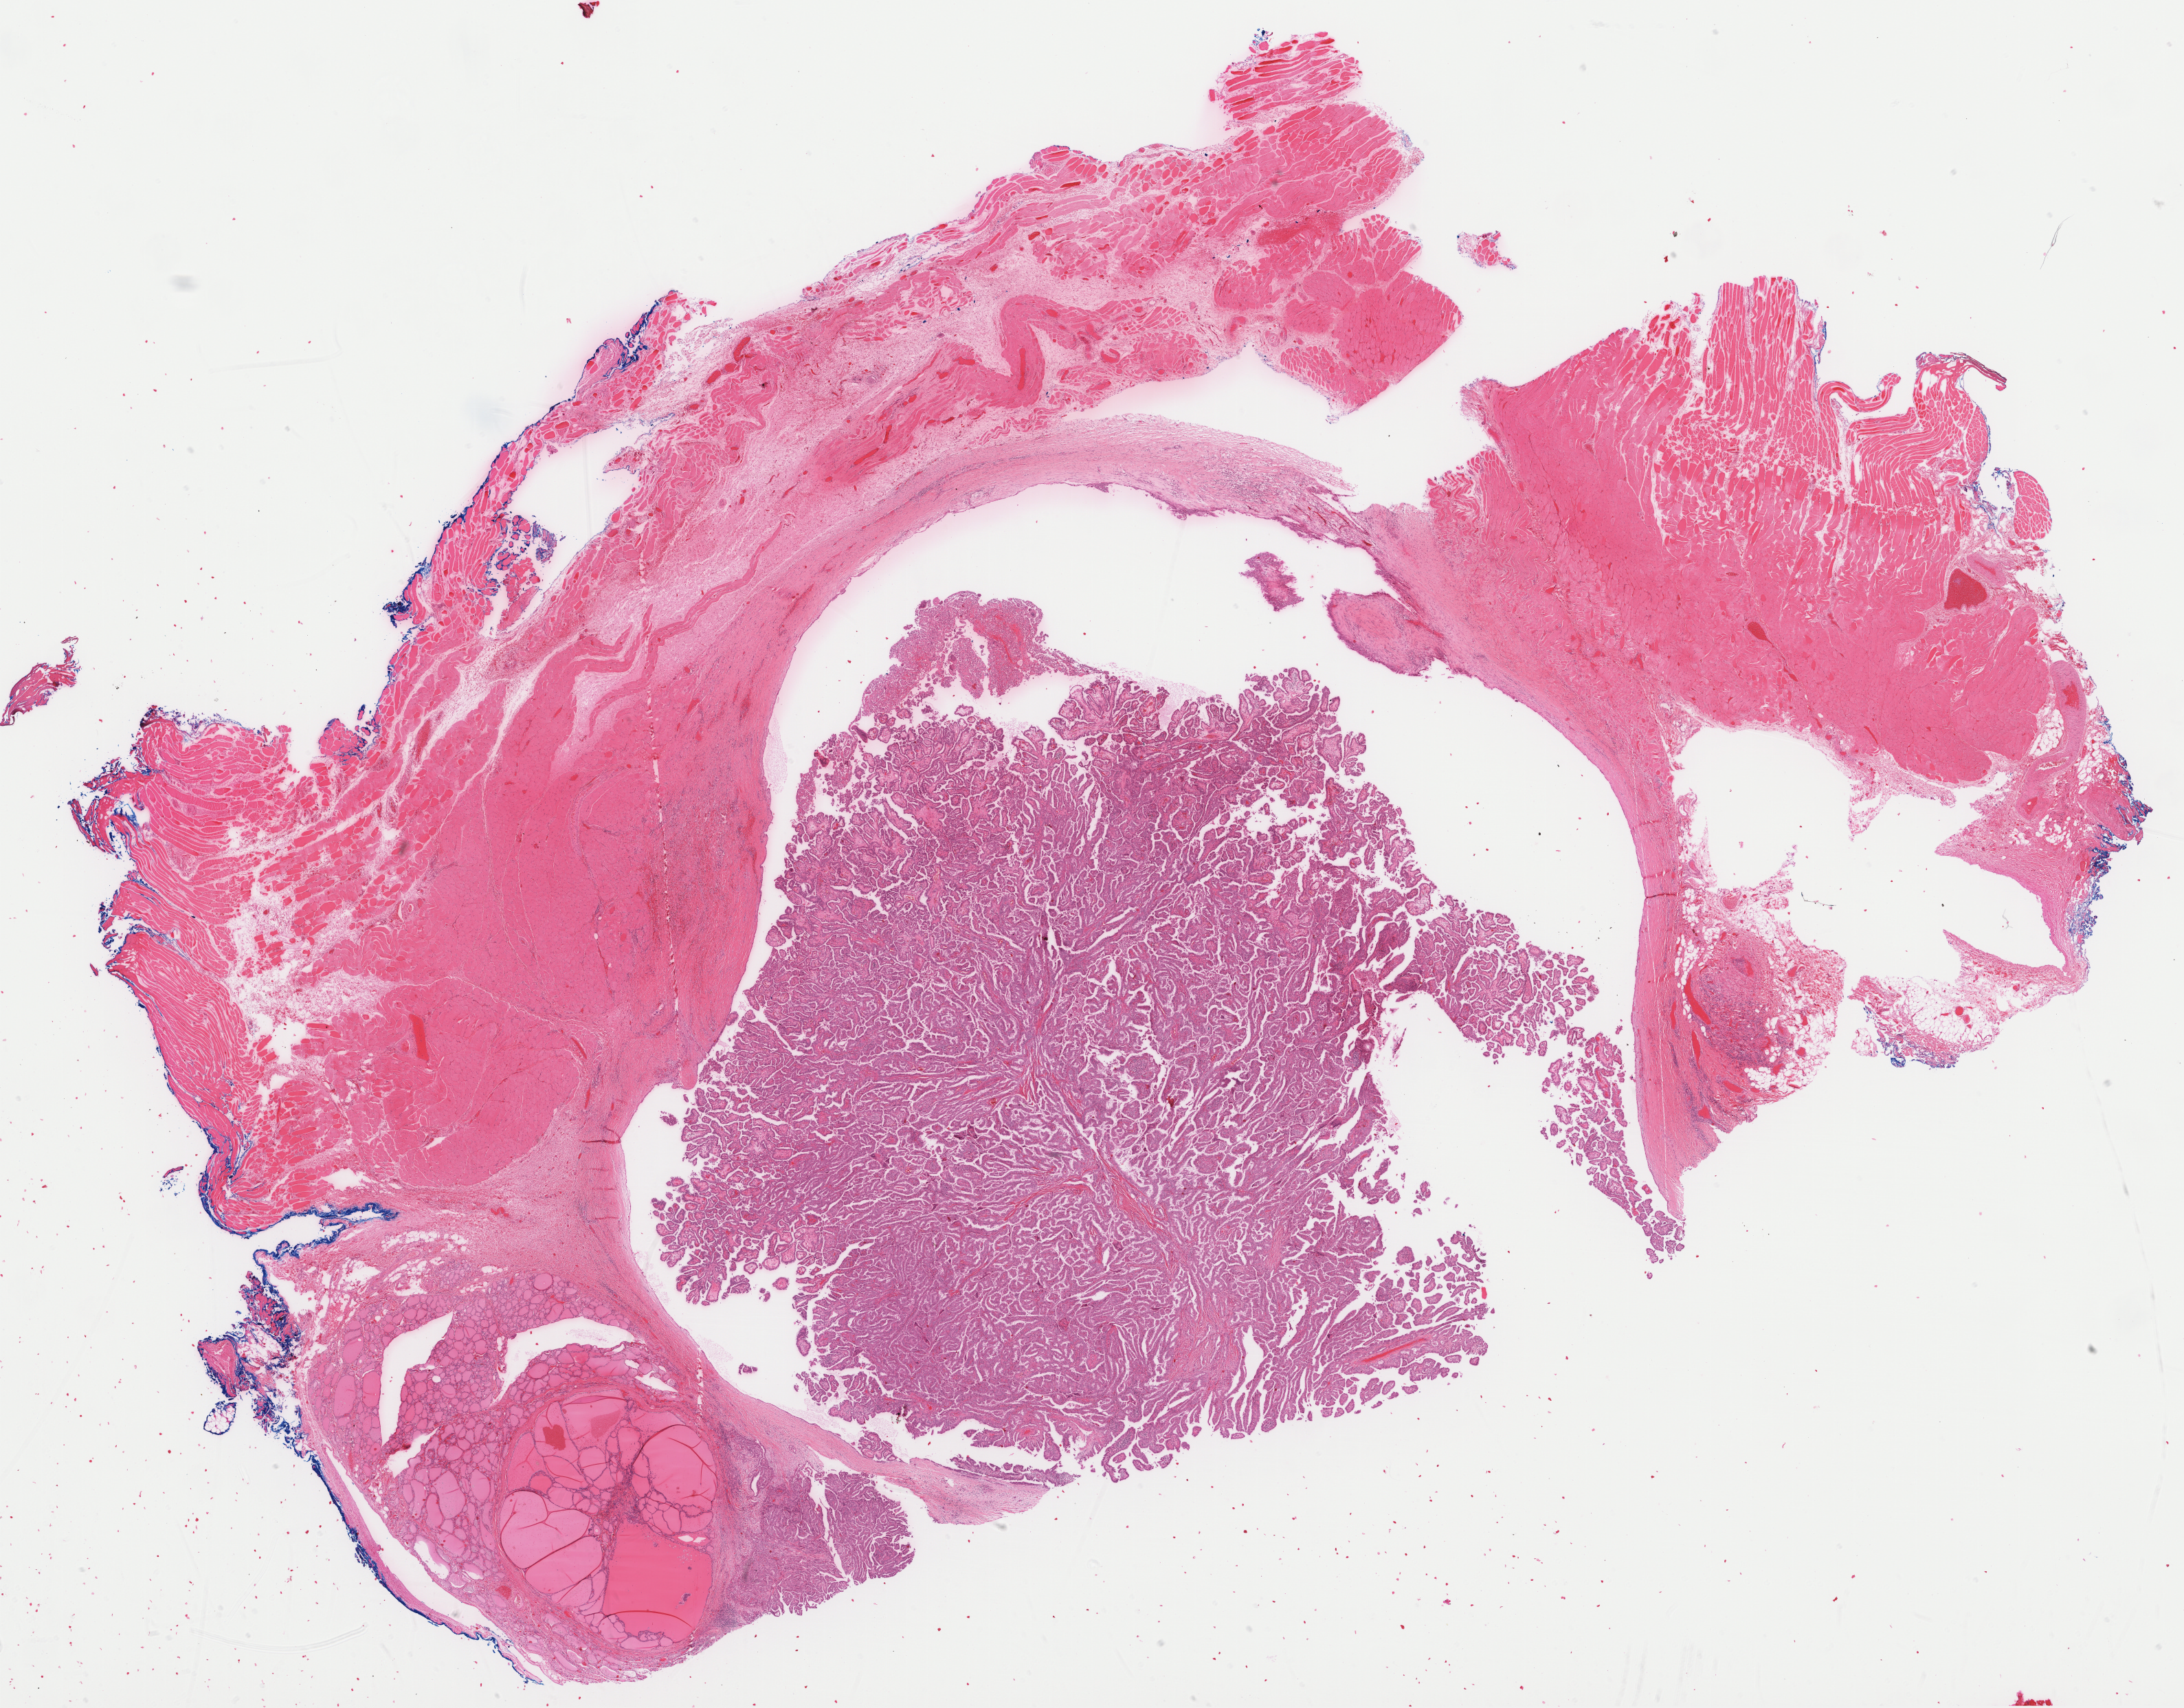
Digitized H&E-stained tissue section (whole slide), shown as a low-resolution overview of the whole scanned area (about 25.8 x 20.1 mm), formalin-fixed paraffin-embedded (FFPE) diagnostic section, sample: primary tumour, thyroid. Male patient; age at initial diagnosis 49 years.
- pathologic diagnosis: Papillary adenocarcinoma, NOS (thyroid gland)
- lymph nodes positive (case pathology): 3 of 5 examined
- AJCC pathologic stage: IVA (7th edition)